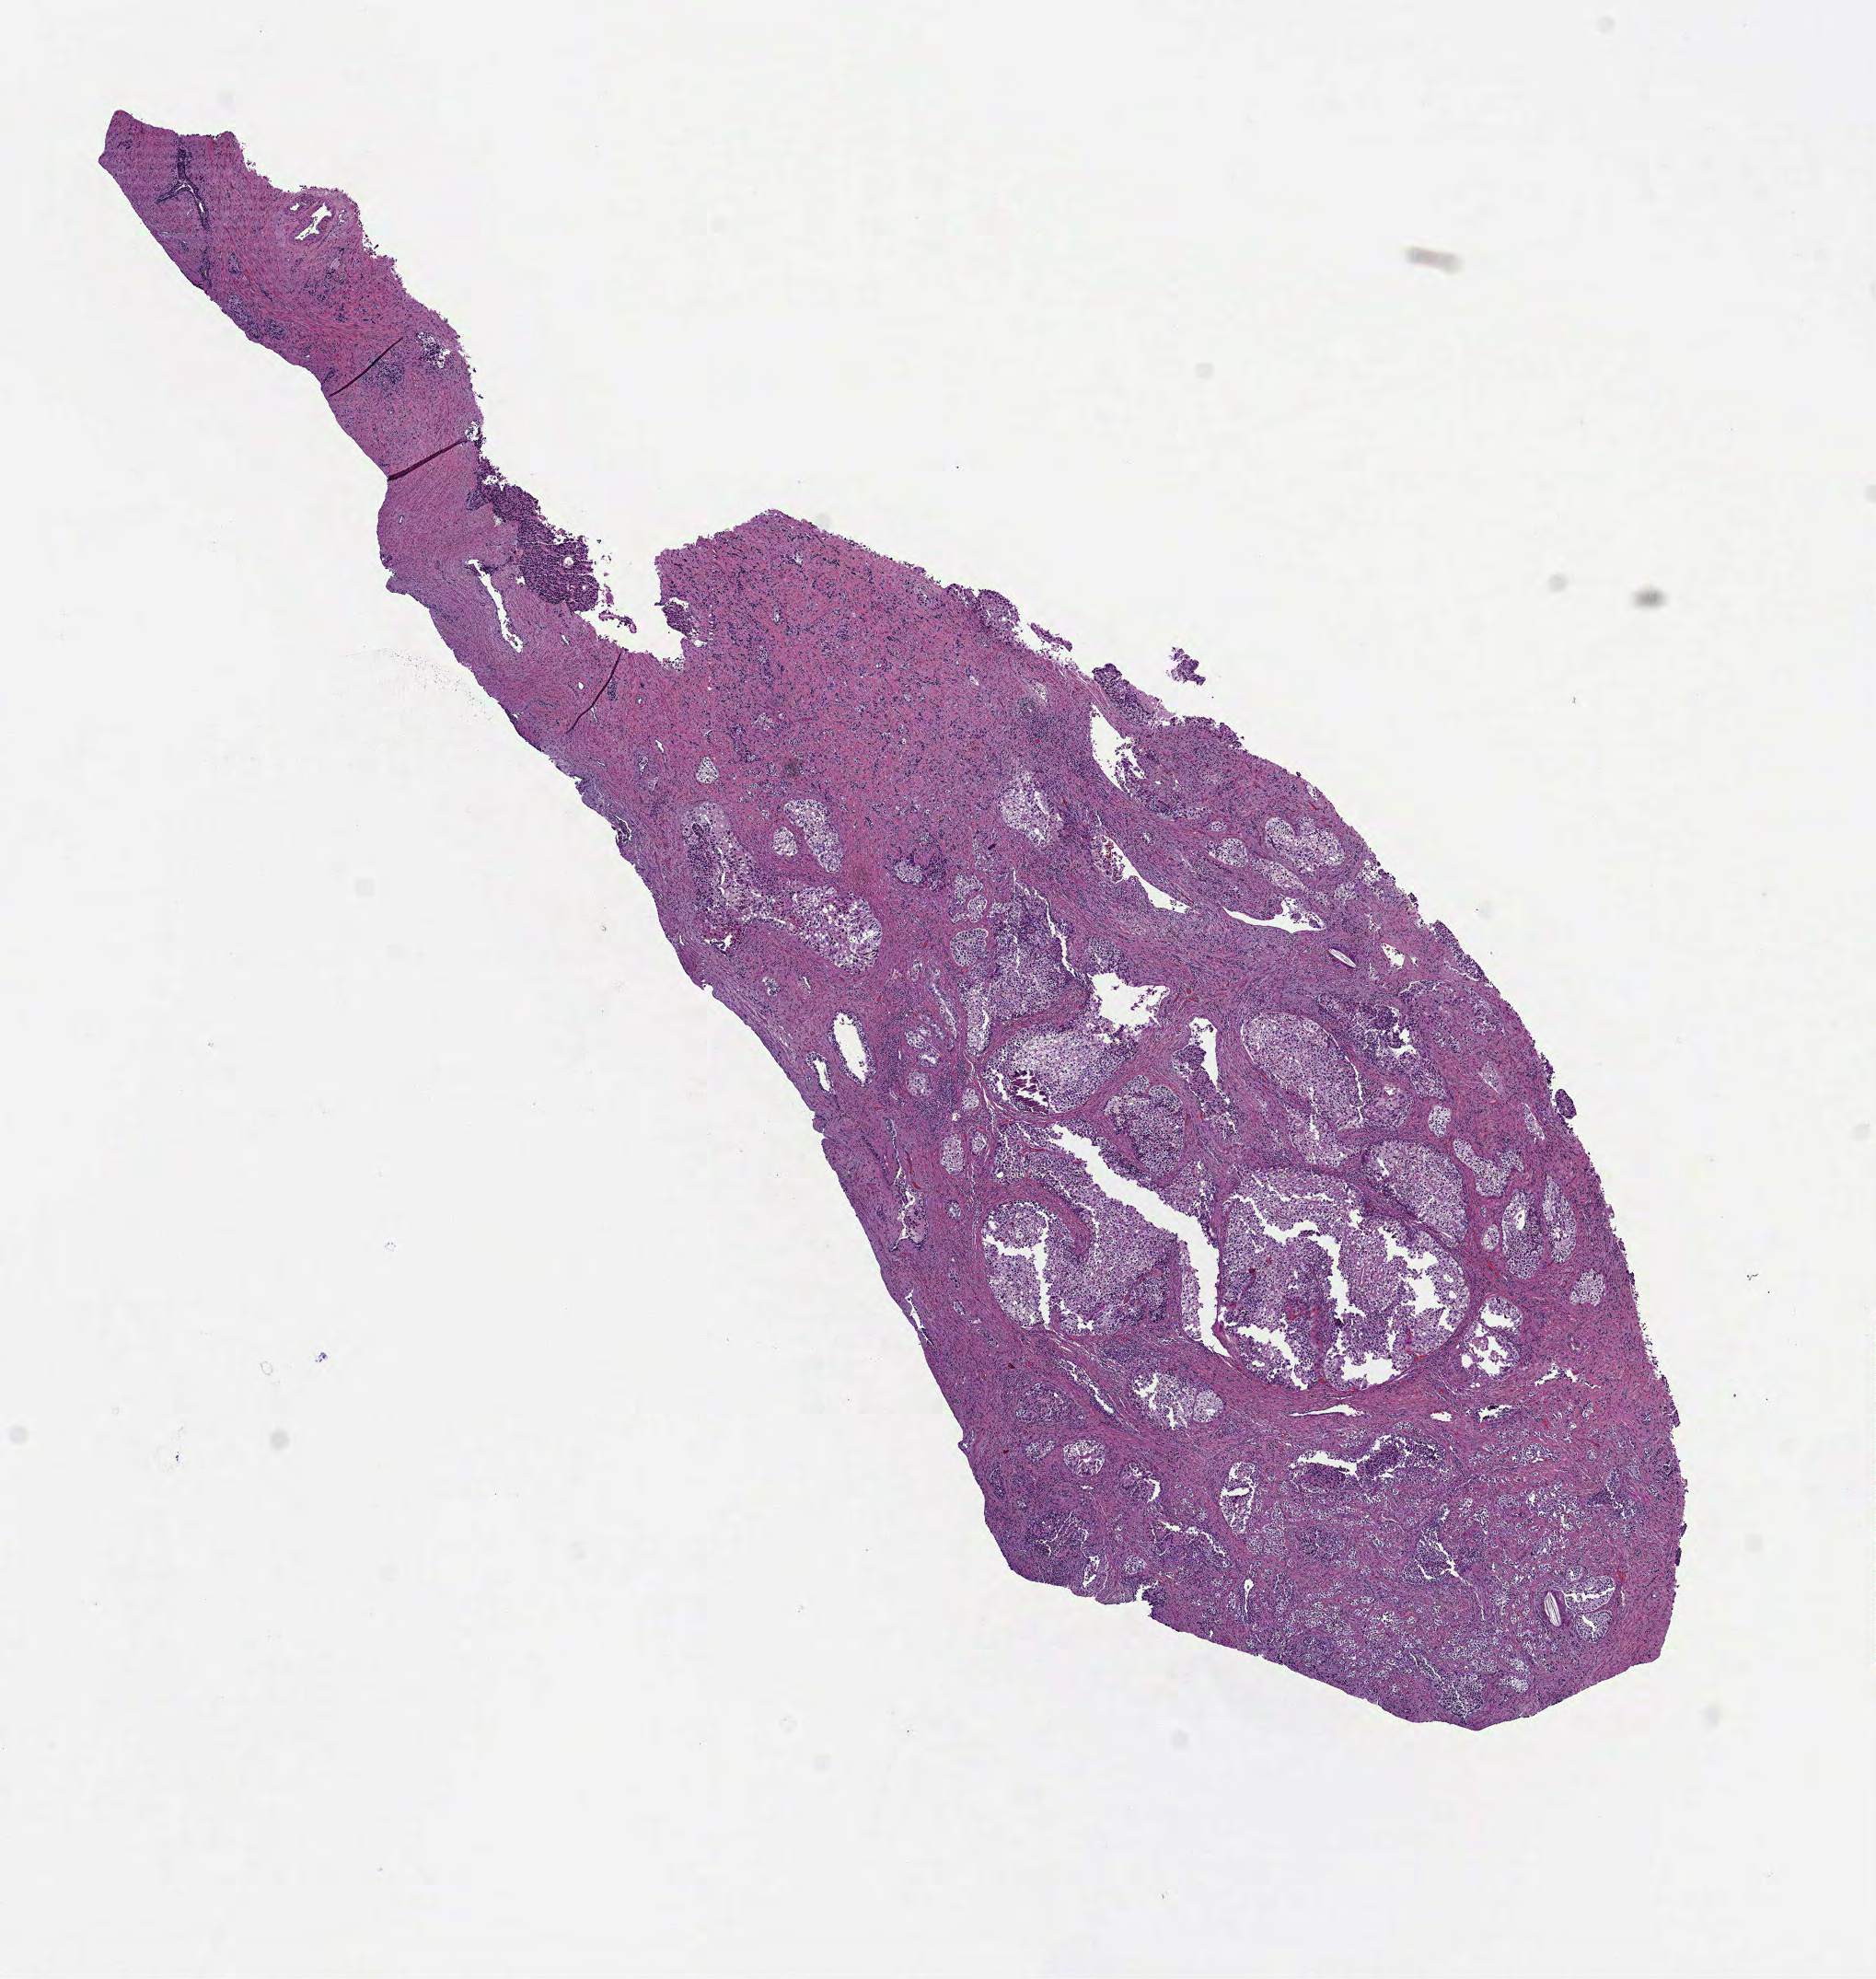
Digitized H&E-stained tissue section (whole slide), low-resolution overview of the scanned area, about 8.2 x 8.7 mm (acquisition: 40x scan). Formalin-fixed paraffin-embedded (FFPE) diagnostic section. Sample: primary tumour, prostate. Patient: male, age at initial diagnosis 64 years. Gleason score: 9 (5+4).
Diagnosis: Adenocarcinoma, NOS (prostate gland).